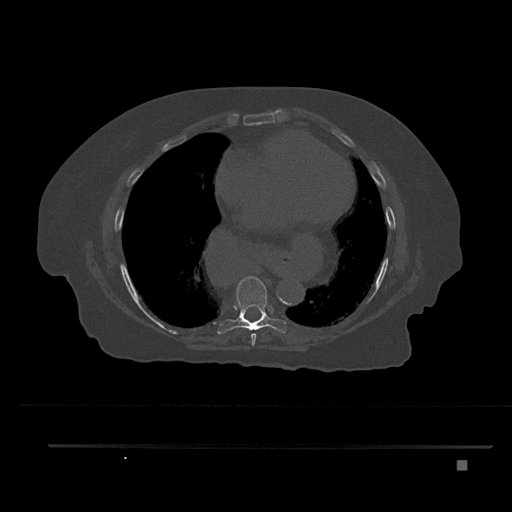
CT including the spine, one axial slice; slice 448 of 797 in the series (ordered by position); reconstruction kernel Br40s/3; bone window (W 1800 / L 400 HU); 512 × 512 image matrix. Patient: female, 76 years. Case-level facts recorded for this patient, not image findings: primary cancer: lung; vertebrae with lytic lesions (as recorded): T11, L3.
Outlined on this slice (semi-automatic segmentation, software-assisted and operator-edited):
- T7 vertebra: bounding box (x1, y1, x2, y2) in pixels: (251, 333, 256, 346)
- T8 vertebra: (217, 276, 287, 334)